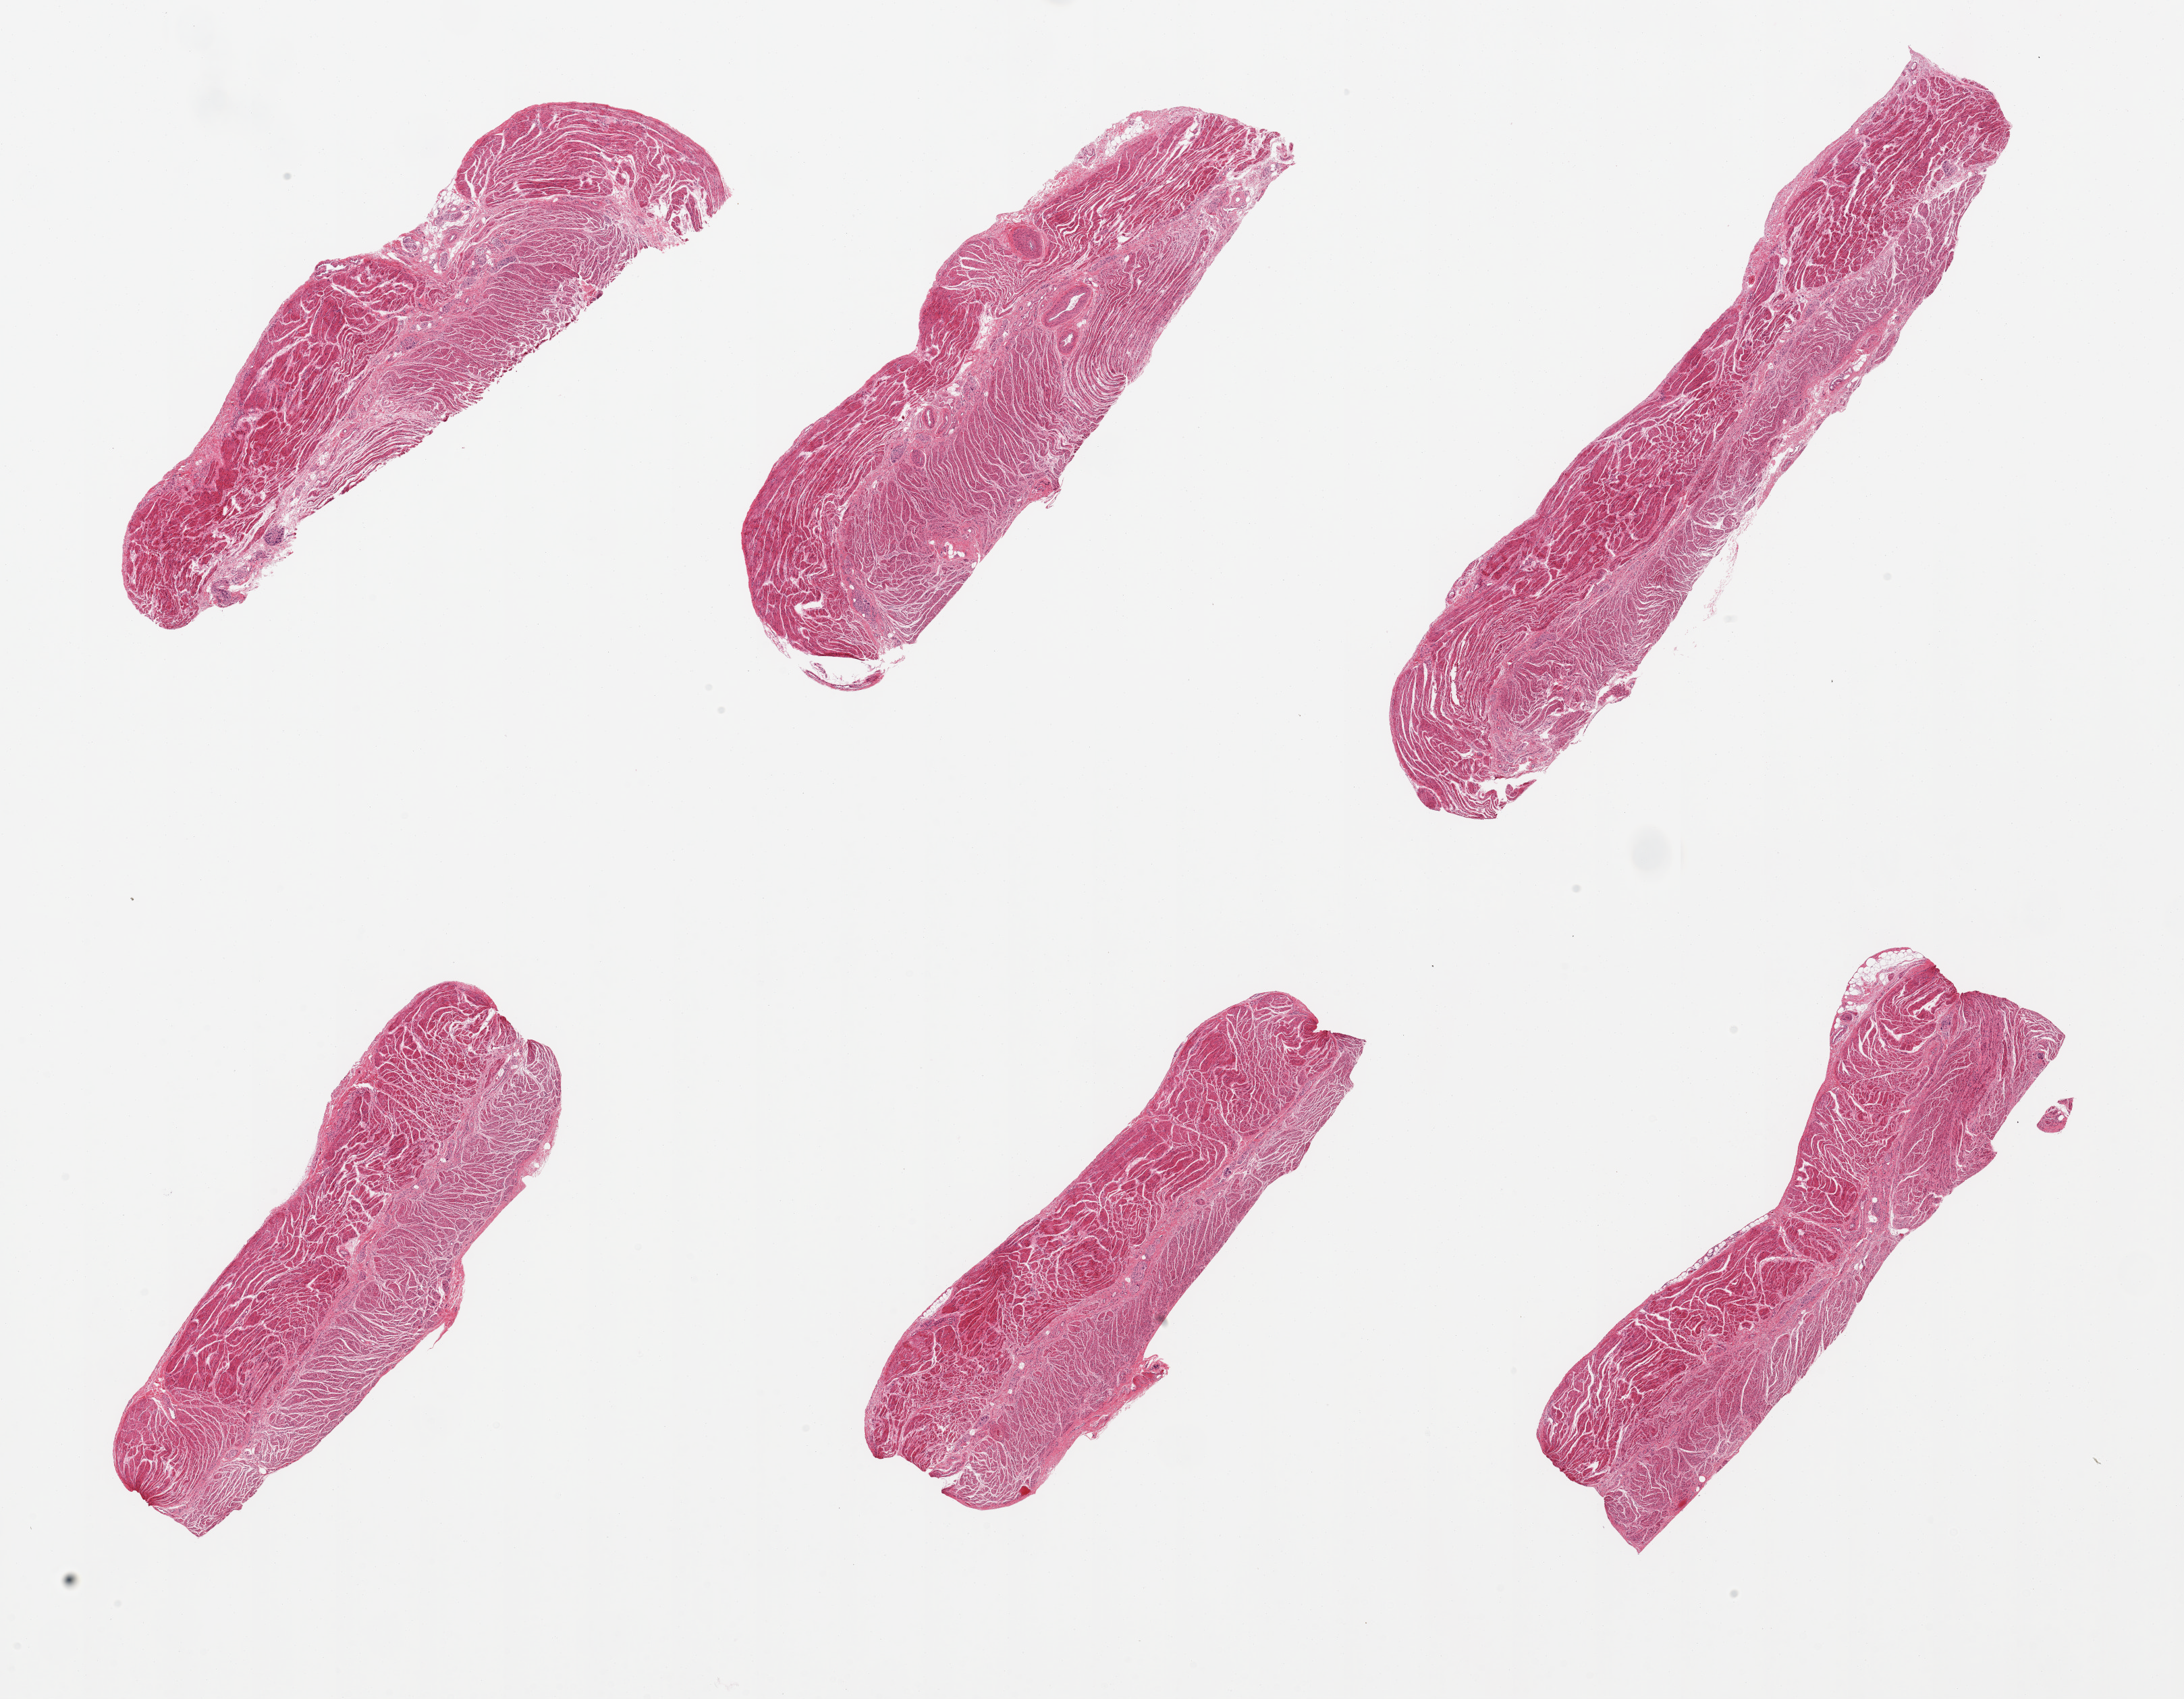
Hematoxylin and eosin (H&E) whole-slide image — shown as a low-resolution overview of the whole scanned area (about 25.6 x 19.9 mm), PAXgene-fixed paraffin-embedded (PFPE) section, section of gastroesophageal junction (target tissue), donor tissue sample. Male donor.
- review note (as recorded): 6 pieces, all target muscularis